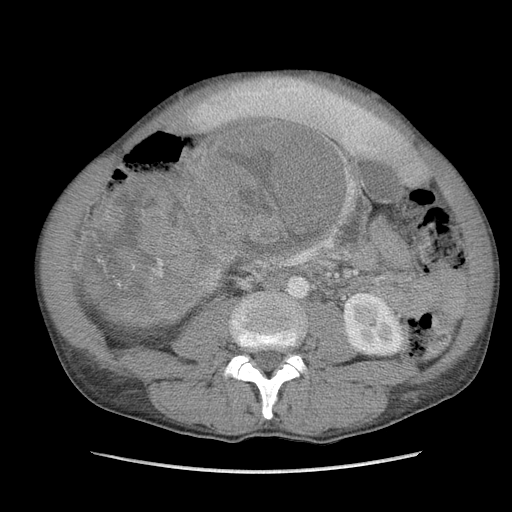
Contrast-enhanced abdominal CT, one axial slice. Slice 46 of 115 in the series (ordered by position). Soft-tissue window (W 400 / L 40 HU). 512 × 512 image matrix, field of view 360 × 360 mm. Male patient. From the clinical record (not read from this slice): diagnosis: adrenocortical carcinoma; tumour side: right adrenal; Ki-67 index: 13 %; stage (as recorded): 3.
Annotated regions visible in this slice (semi-automatically segmented with operator editing):
- mass: bounding box <91,123,341,320> (left, top, right, bottom; pixels)